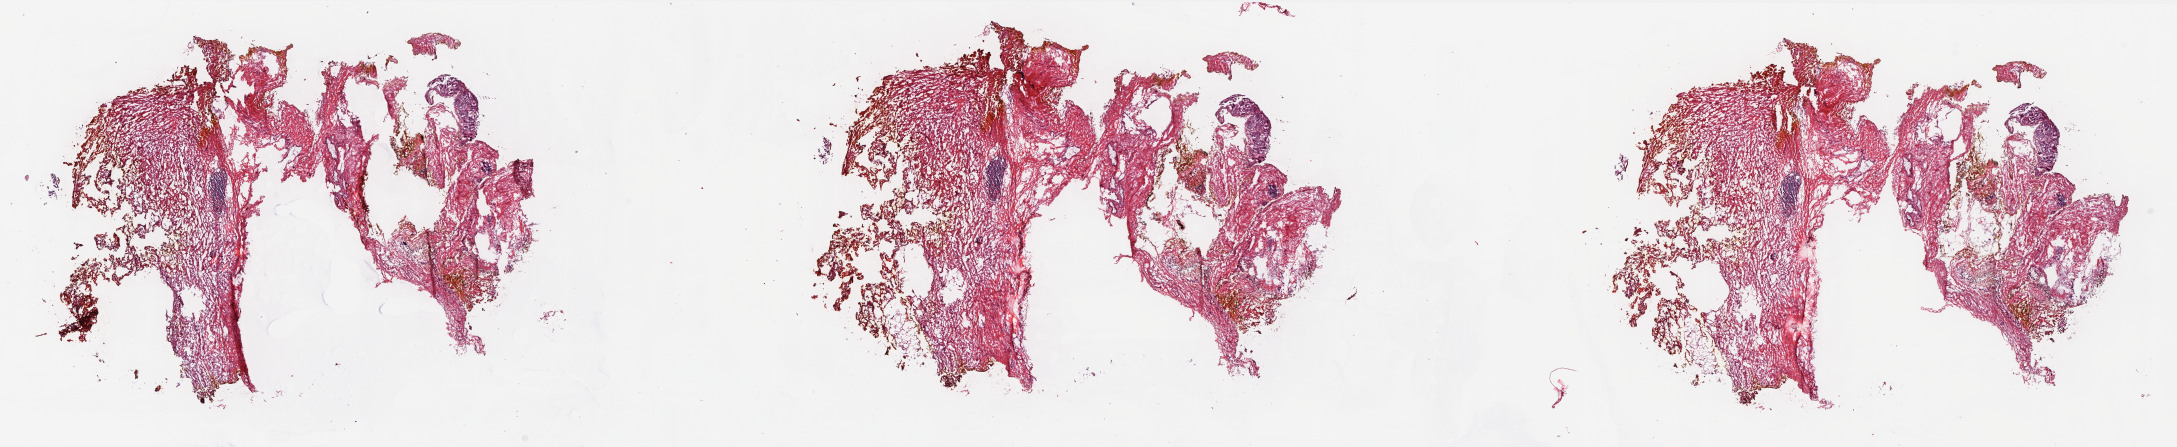
Digitized Hematoxylin and eosin (H&E) stained tissue section (whole slide) — shown as a low-resolution overview of the whole scanned area (about 35.1 x 7.2 mm, acquisition: 20x scan). Frozen section from the top of the tissue portion. Kidney, solid tissue normal (non-tumour tissue) sample. Male patient; age at initial diagnosis 66 years. Pathologist review of this section (percent, as recorded): tumour cells 0%, tumour nuclei 0%, normal cells 100%, stromal cells 0%, necrosis 0%. Inflammatory infiltration, as recorded: lymphocyte infiltration 2%, monocyte infiltration 0%, neutrophil infiltration 0%.
This section: solid tissue normal sample (biorepository sample class). Patient diagnosis: Papillary adenocarcinoma, NOS.